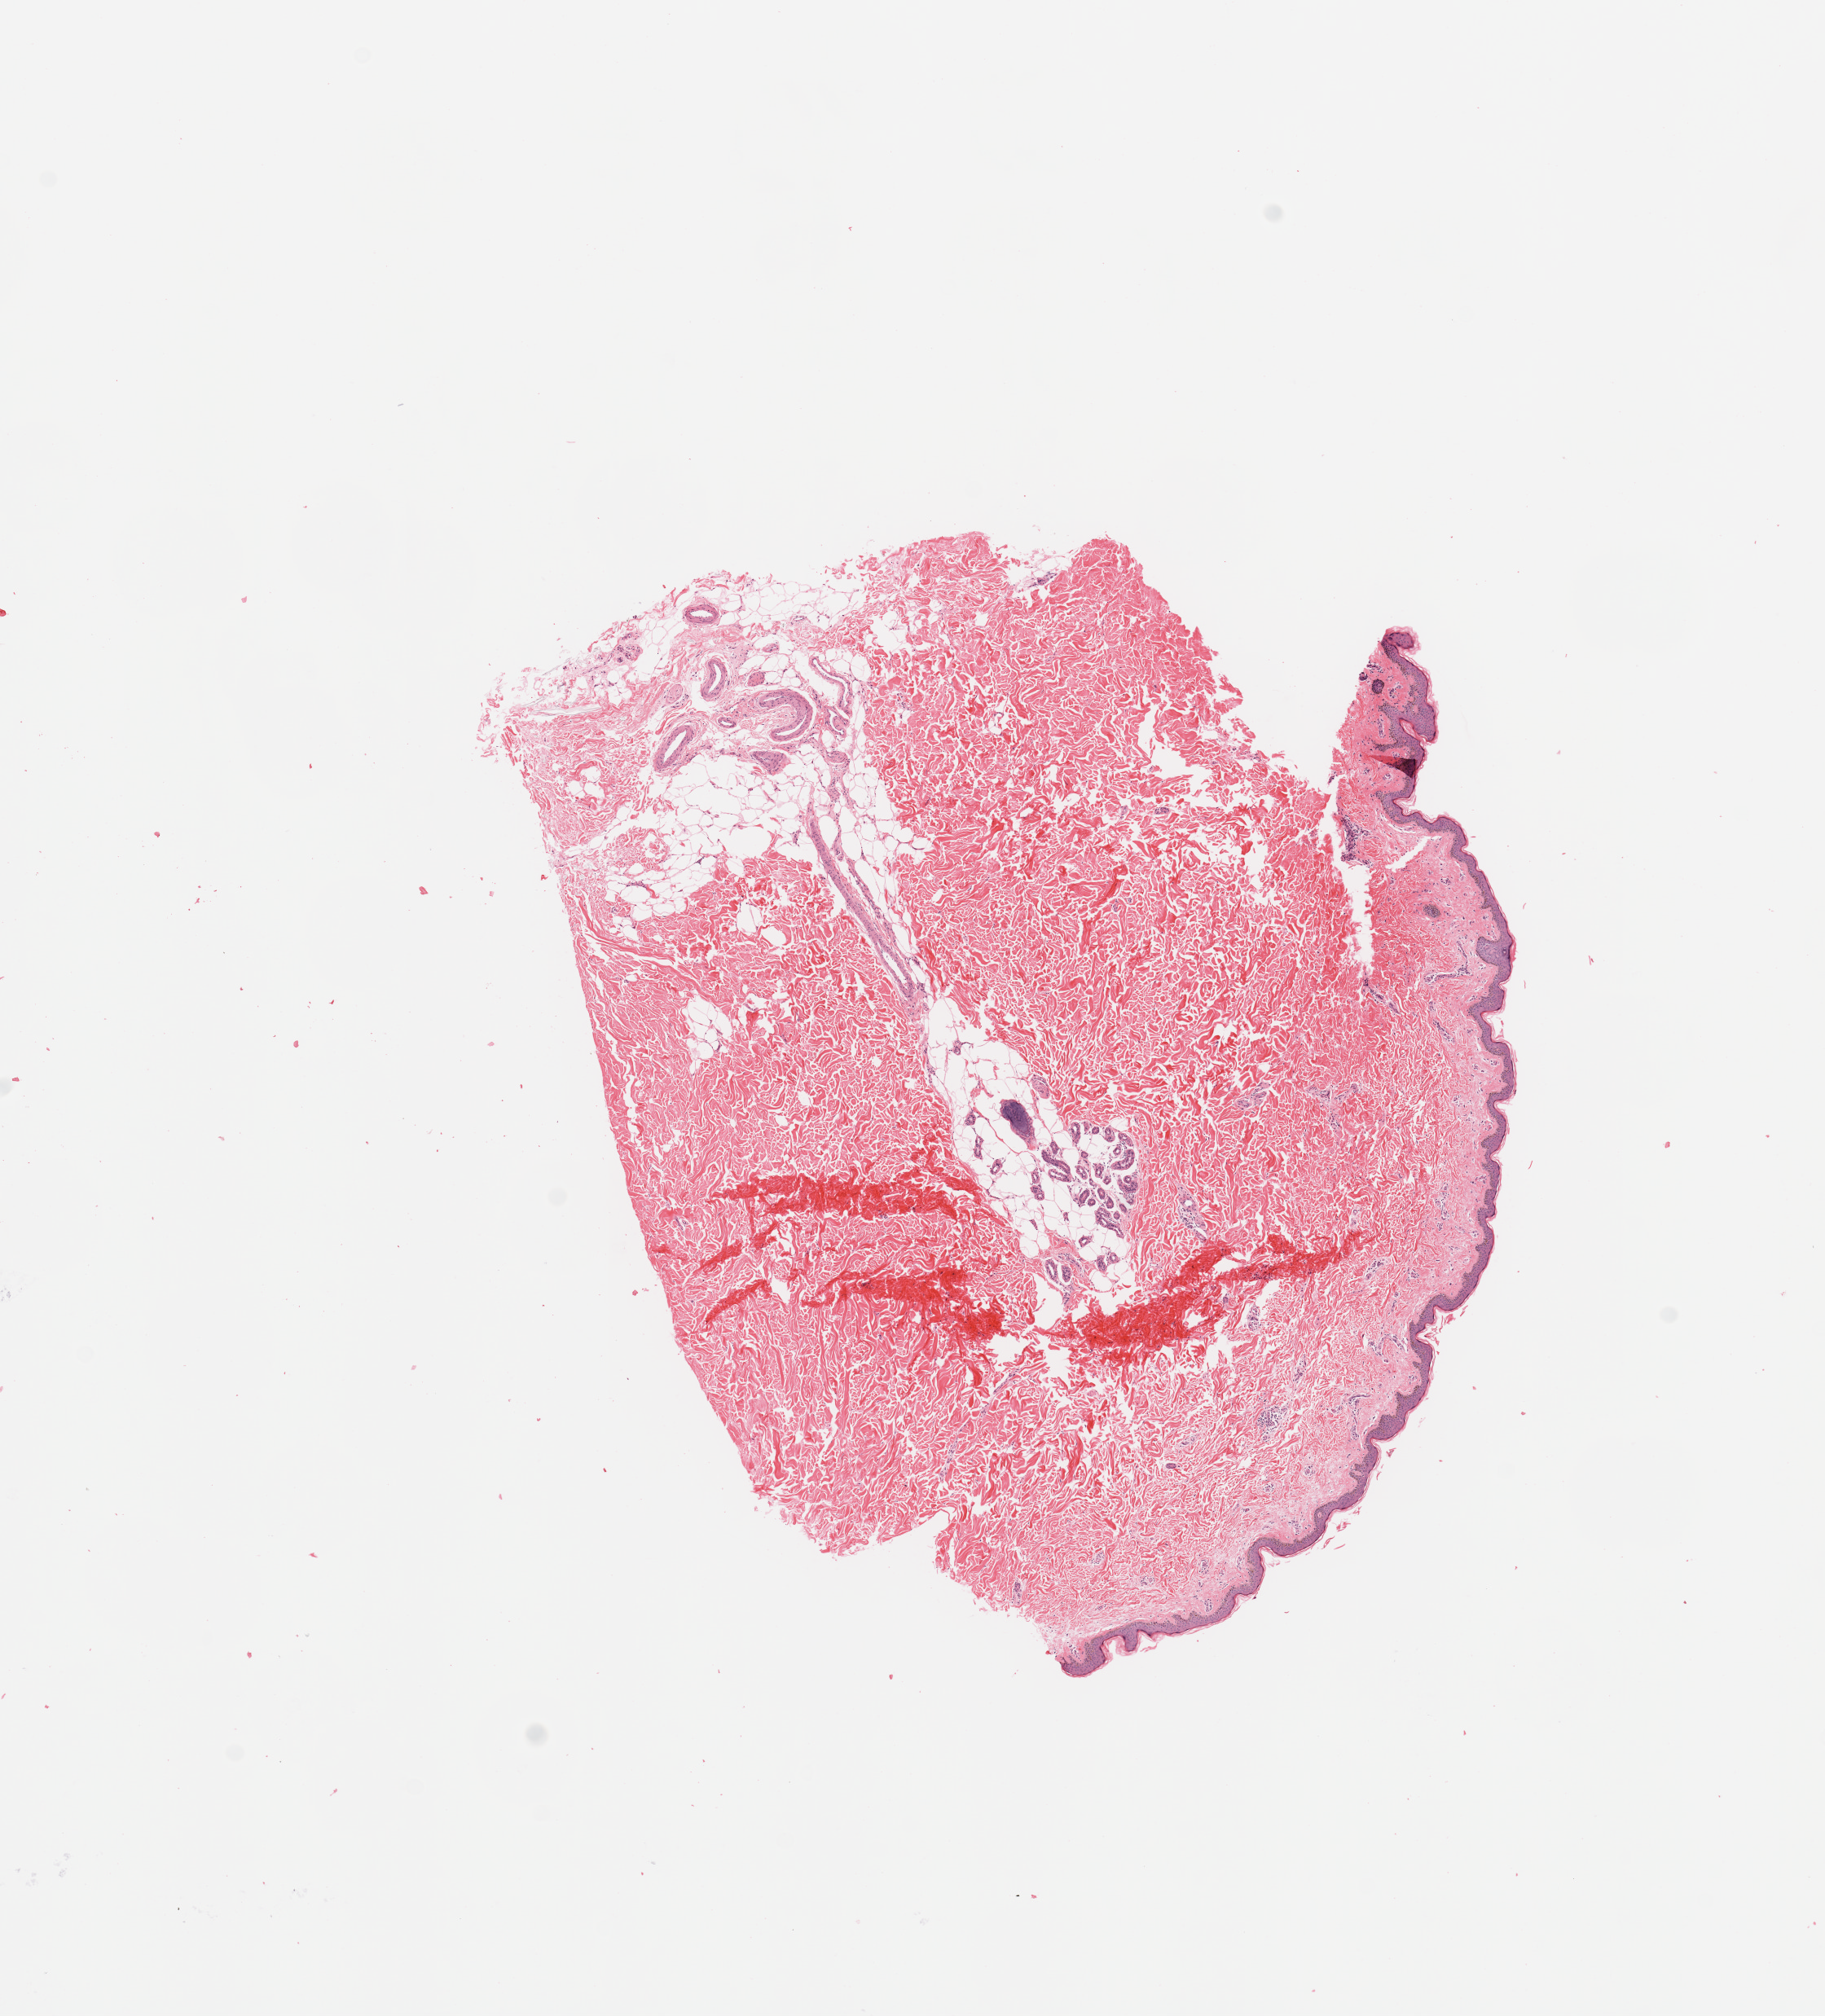
Whole-slide histology image, H&E-stained, shown as a low-resolution overview of the whole scanned area (about 8.9 x 9.8 mm), normal (non-tumour) tissue (melanoma cohort); sampled site not recorded. 45-year-old female patient.
This section: normal (non-tumour) tissue from the same patient. Patient diagnosis (cohort enrolment): cutaneous melanoma (skin).